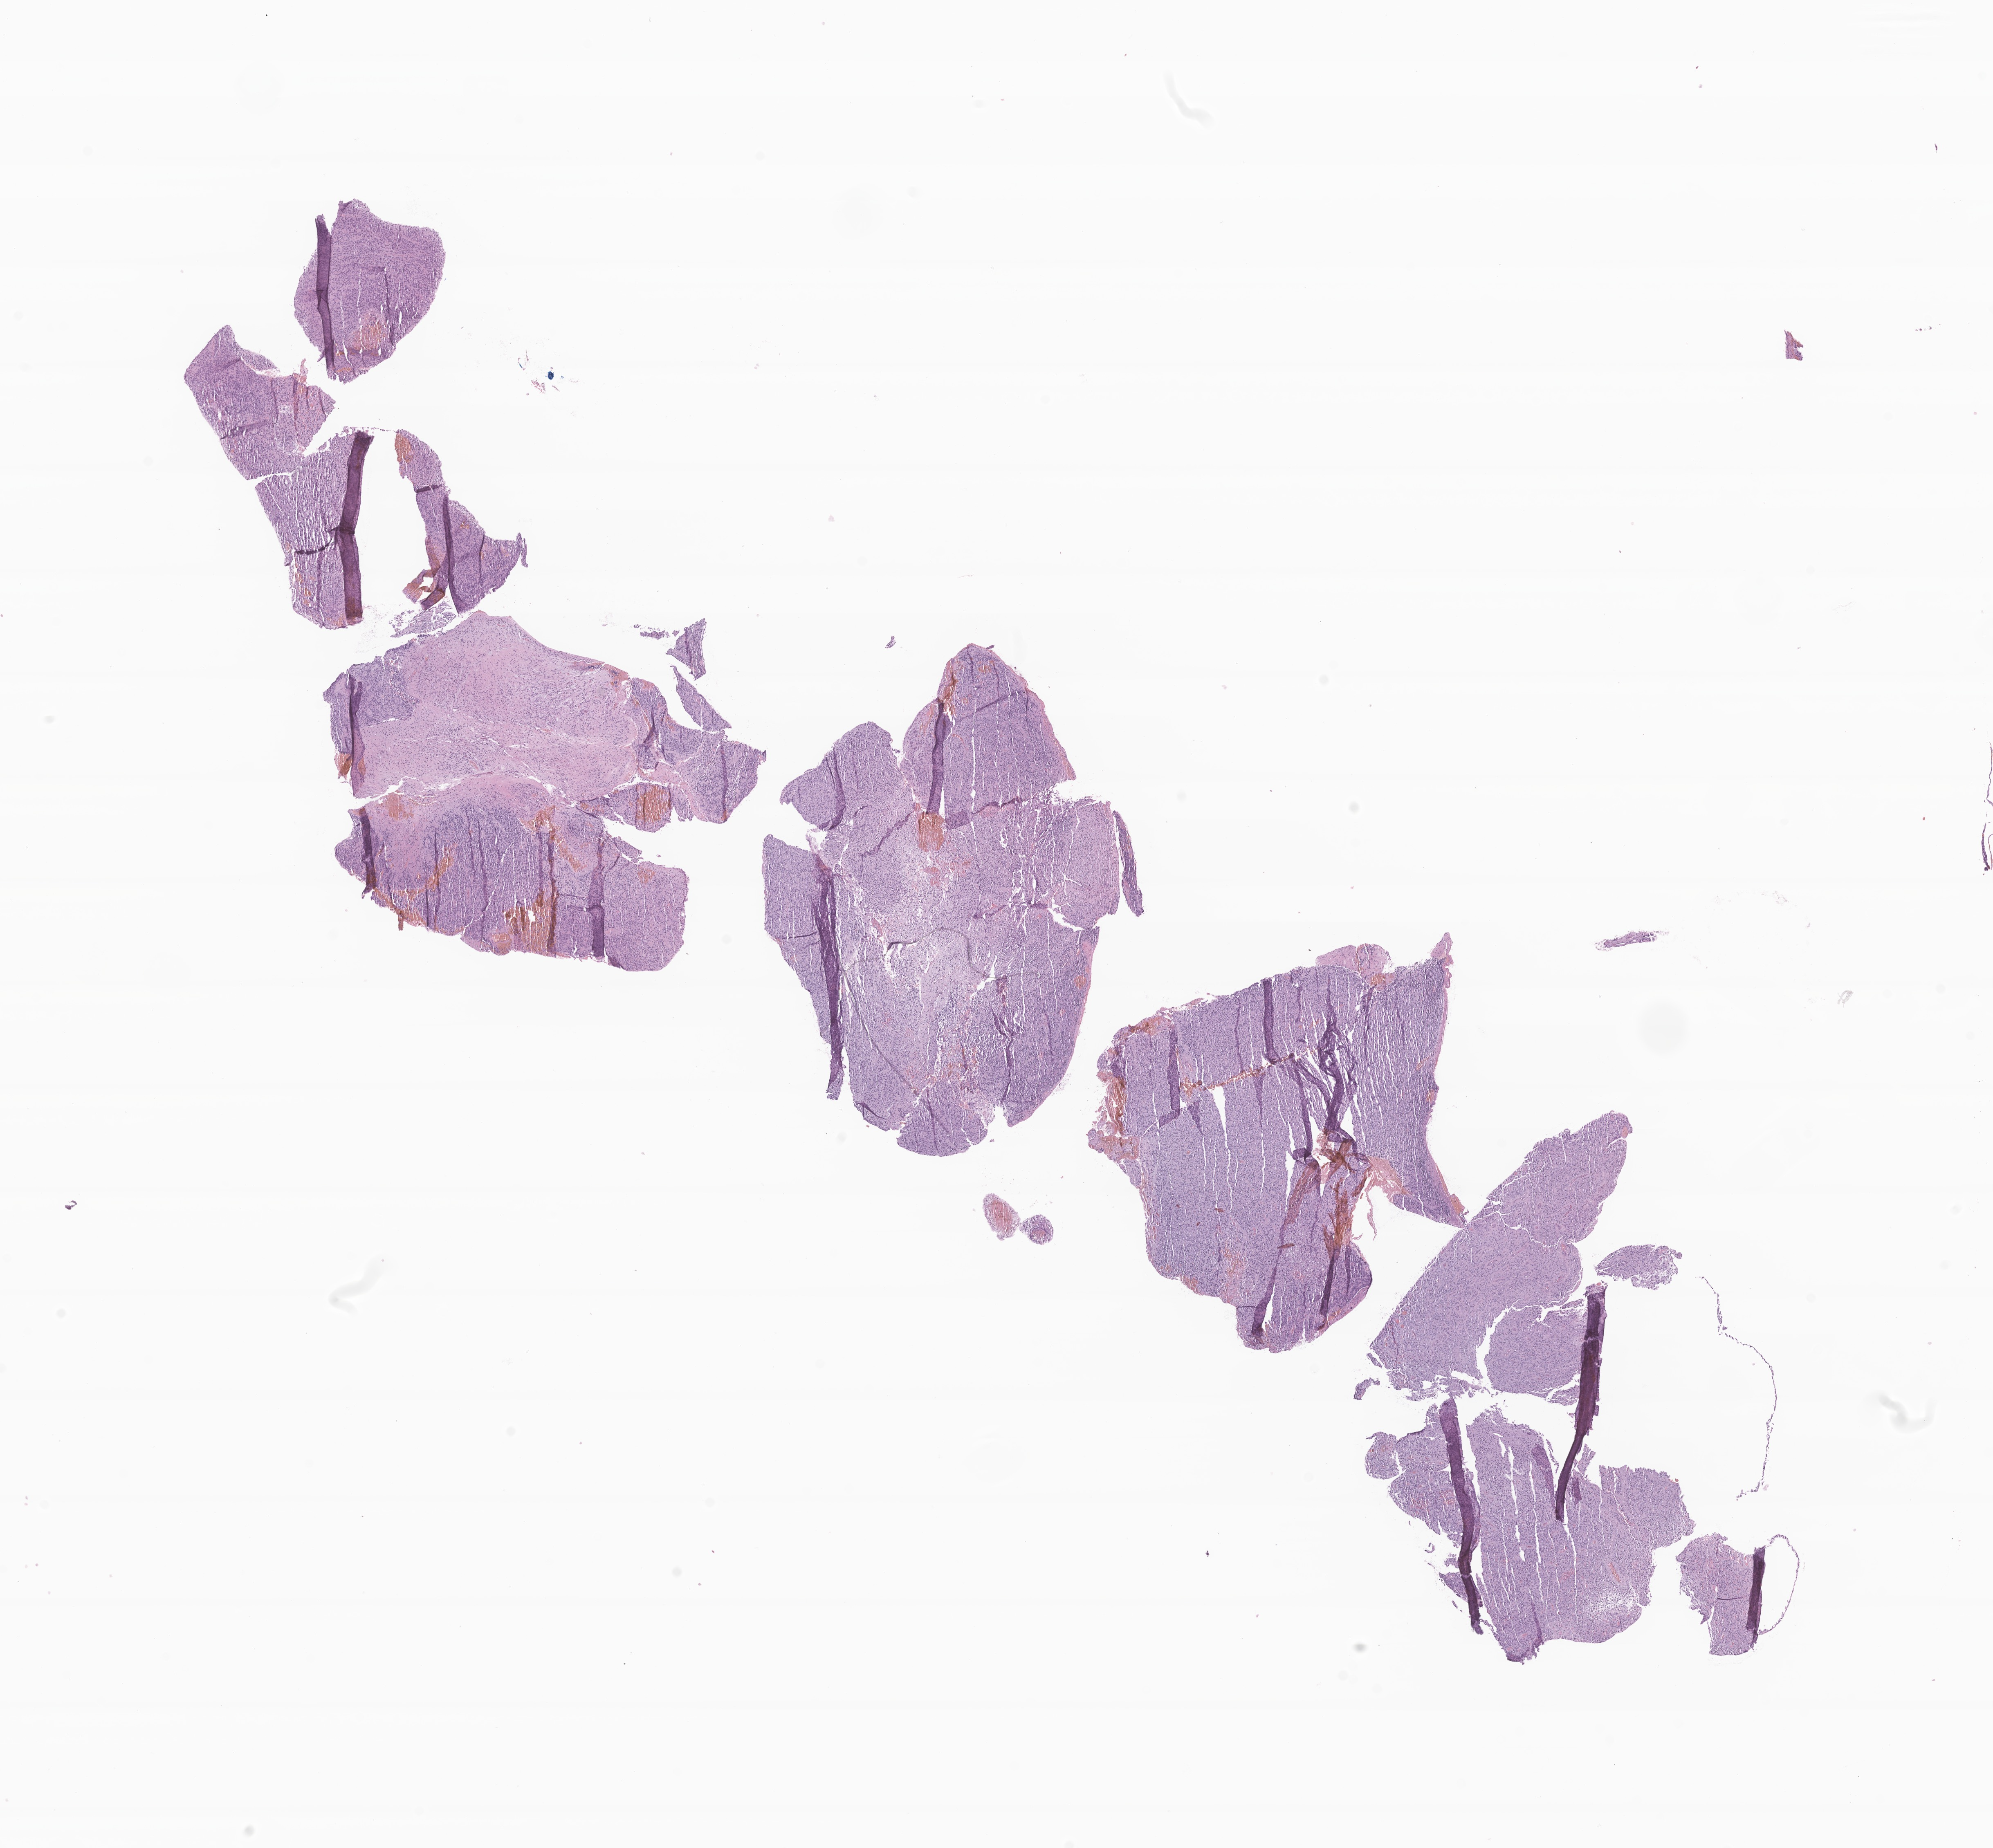
Whole-slide image, hematoxylin and eosin (H&E) stain of tumor tissue from the brain — shown as a low-resolution overview of the whole scanned area (about 20.4 x 18.9 mm), formalin-fixed paraffin-embedded section. Patient male; age 810 days (about 2.2 years).
Diagnosis (ICD-O-3 morphology term): Neoplasm, uncertain whether benign or malignant.